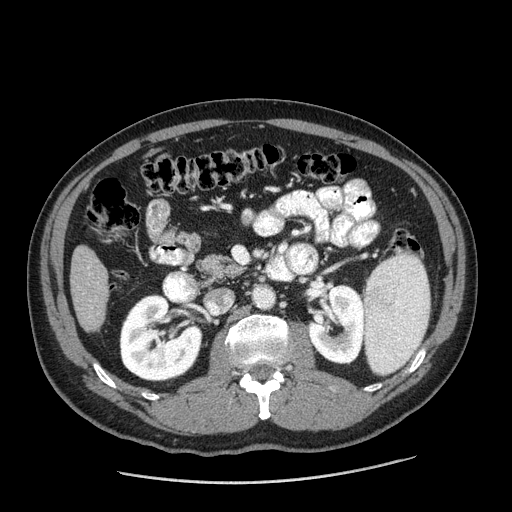
Contrast-enhanced abdominal CT (liver protocol), one axial slice. Slice 59 of 198 in the series (ordered by position). Reconstruction kernel STANDARD. 120 kVp. One of 2 acquisitions stored at this slice position. Soft-tissue window (W 400 / L 40 HU). 2.5 mm slice thickness. 512 × 512 image matrix, field of view 400 × 400 mm. Case-level facts recorded for this patient, not image findings: diagnosis: hepatocellular carcinoma (patient treated with transarterial chemoembolisation; whether this scan precedes or follows treatment is not stated here); TNM stage (as recorded): Stage-II; Child-Pugh class: A; tumour differentiation: moderately differentiated; tumour nodularity: multinodular.
Structures marked on this image (semi-automatically segmented with operator editing):
- liver parenchyma outside the tumour (the mass and vessels are separate outlines, so this box may not span the whole liver): box from (x=70, y=246) to (x=108, y=331) px